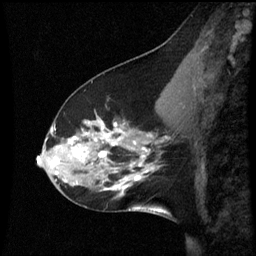
Breast MRI (dynamic contrast-enhanced), one sagittal slice; position 22 of 60 along the scan axis; dynamic contrast-enhanced series, image 2 of 3 at this slice position (ordered by acquisition); 1.5 T; TE 4.2 ms, TR 8.9 ms; 2 mm slice thickness; 256 × 256 image matrix, field of view 200 × 200 mm. Patient: female, 45 years. Case-level facts recorded for this patient, not image findings: setting: breast cancer imaged before/during neoadjuvant chemotherapy; receptor status: HR-positive, HER2-negative.
Structures marked on this image (semi-automatic segmentation, software-assisted and operator-edited):
- analysis volume of interest (the breast-tissue region the enhancement analysis was run in; not a lesion): bounding box [x1, y1, x2, y2] px = [46, 94, 171, 205]
- tumour enhancement mask (voxels above the 70 % enhancement threshold inside the analysis volume of interest): [52, 124, 167, 183]